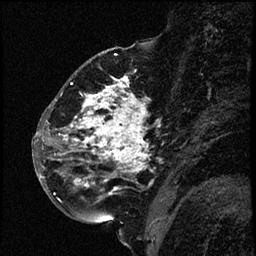
Breast MRI (dynamic contrast-enhanced), one sagittal slice. Dynamic contrast-enhanced study with each time point stored as its own series, time point 2 of 3 at this slice position (early post-contrast, ordered by acquisition time). 1.5 T. TE 4.2 ms, TR 17.6 ms. 2 mm slice thickness. 256 × 256 image matrix, field of view 200 × 200 mm. Female patient. From the clinical record (not read from this slice): setting: breast cancer imaged before/during neoadjuvant chemotherapy; receptor status: HER2-positive.
Structures marked on this image (semi-automatic segmentation, software-assisted and operator-edited):
- analysis volume of interest (the breast-tissue region the enhancement analysis was run in; not a lesion): box from (x=52, y=69) to (x=169, y=209) px
- tumour enhancement mask (voxels above the 100 % enhancement threshold inside the analysis volume of interest): (x=54, y=76)–(x=150, y=195)